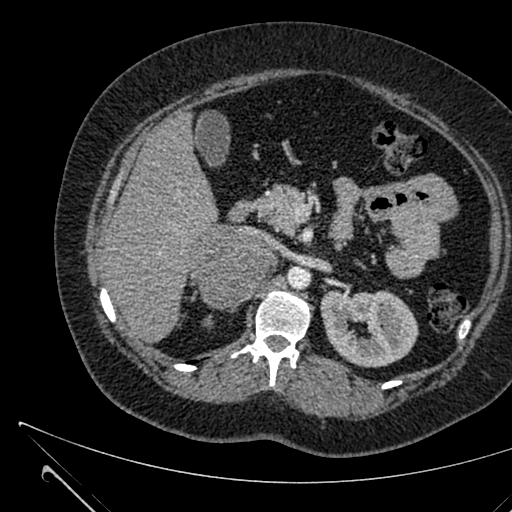
Contrast-enhanced abdominal CT, one axial slice; position 395 of 731 along the scan axis; intravenous contrast given; soft-tissue window (W 400 / L 40 HU); 1 mm slice thickness; 512 × 512 image matrix, field of view 376 × 376 mm. Female patient, age 36 years. From the clinical record (not read from this slice): diagnosis: adrenocortical carcinoma; tumour side: right adrenal; tumour size at pathology: 10 cm; Ki-67 index: 20 %; stage (as recorded): 4.
Structures marked on this image (semi-automatically segmented with operator editing):
- mass: box from (x=190, y=225) to (x=272, y=308) px